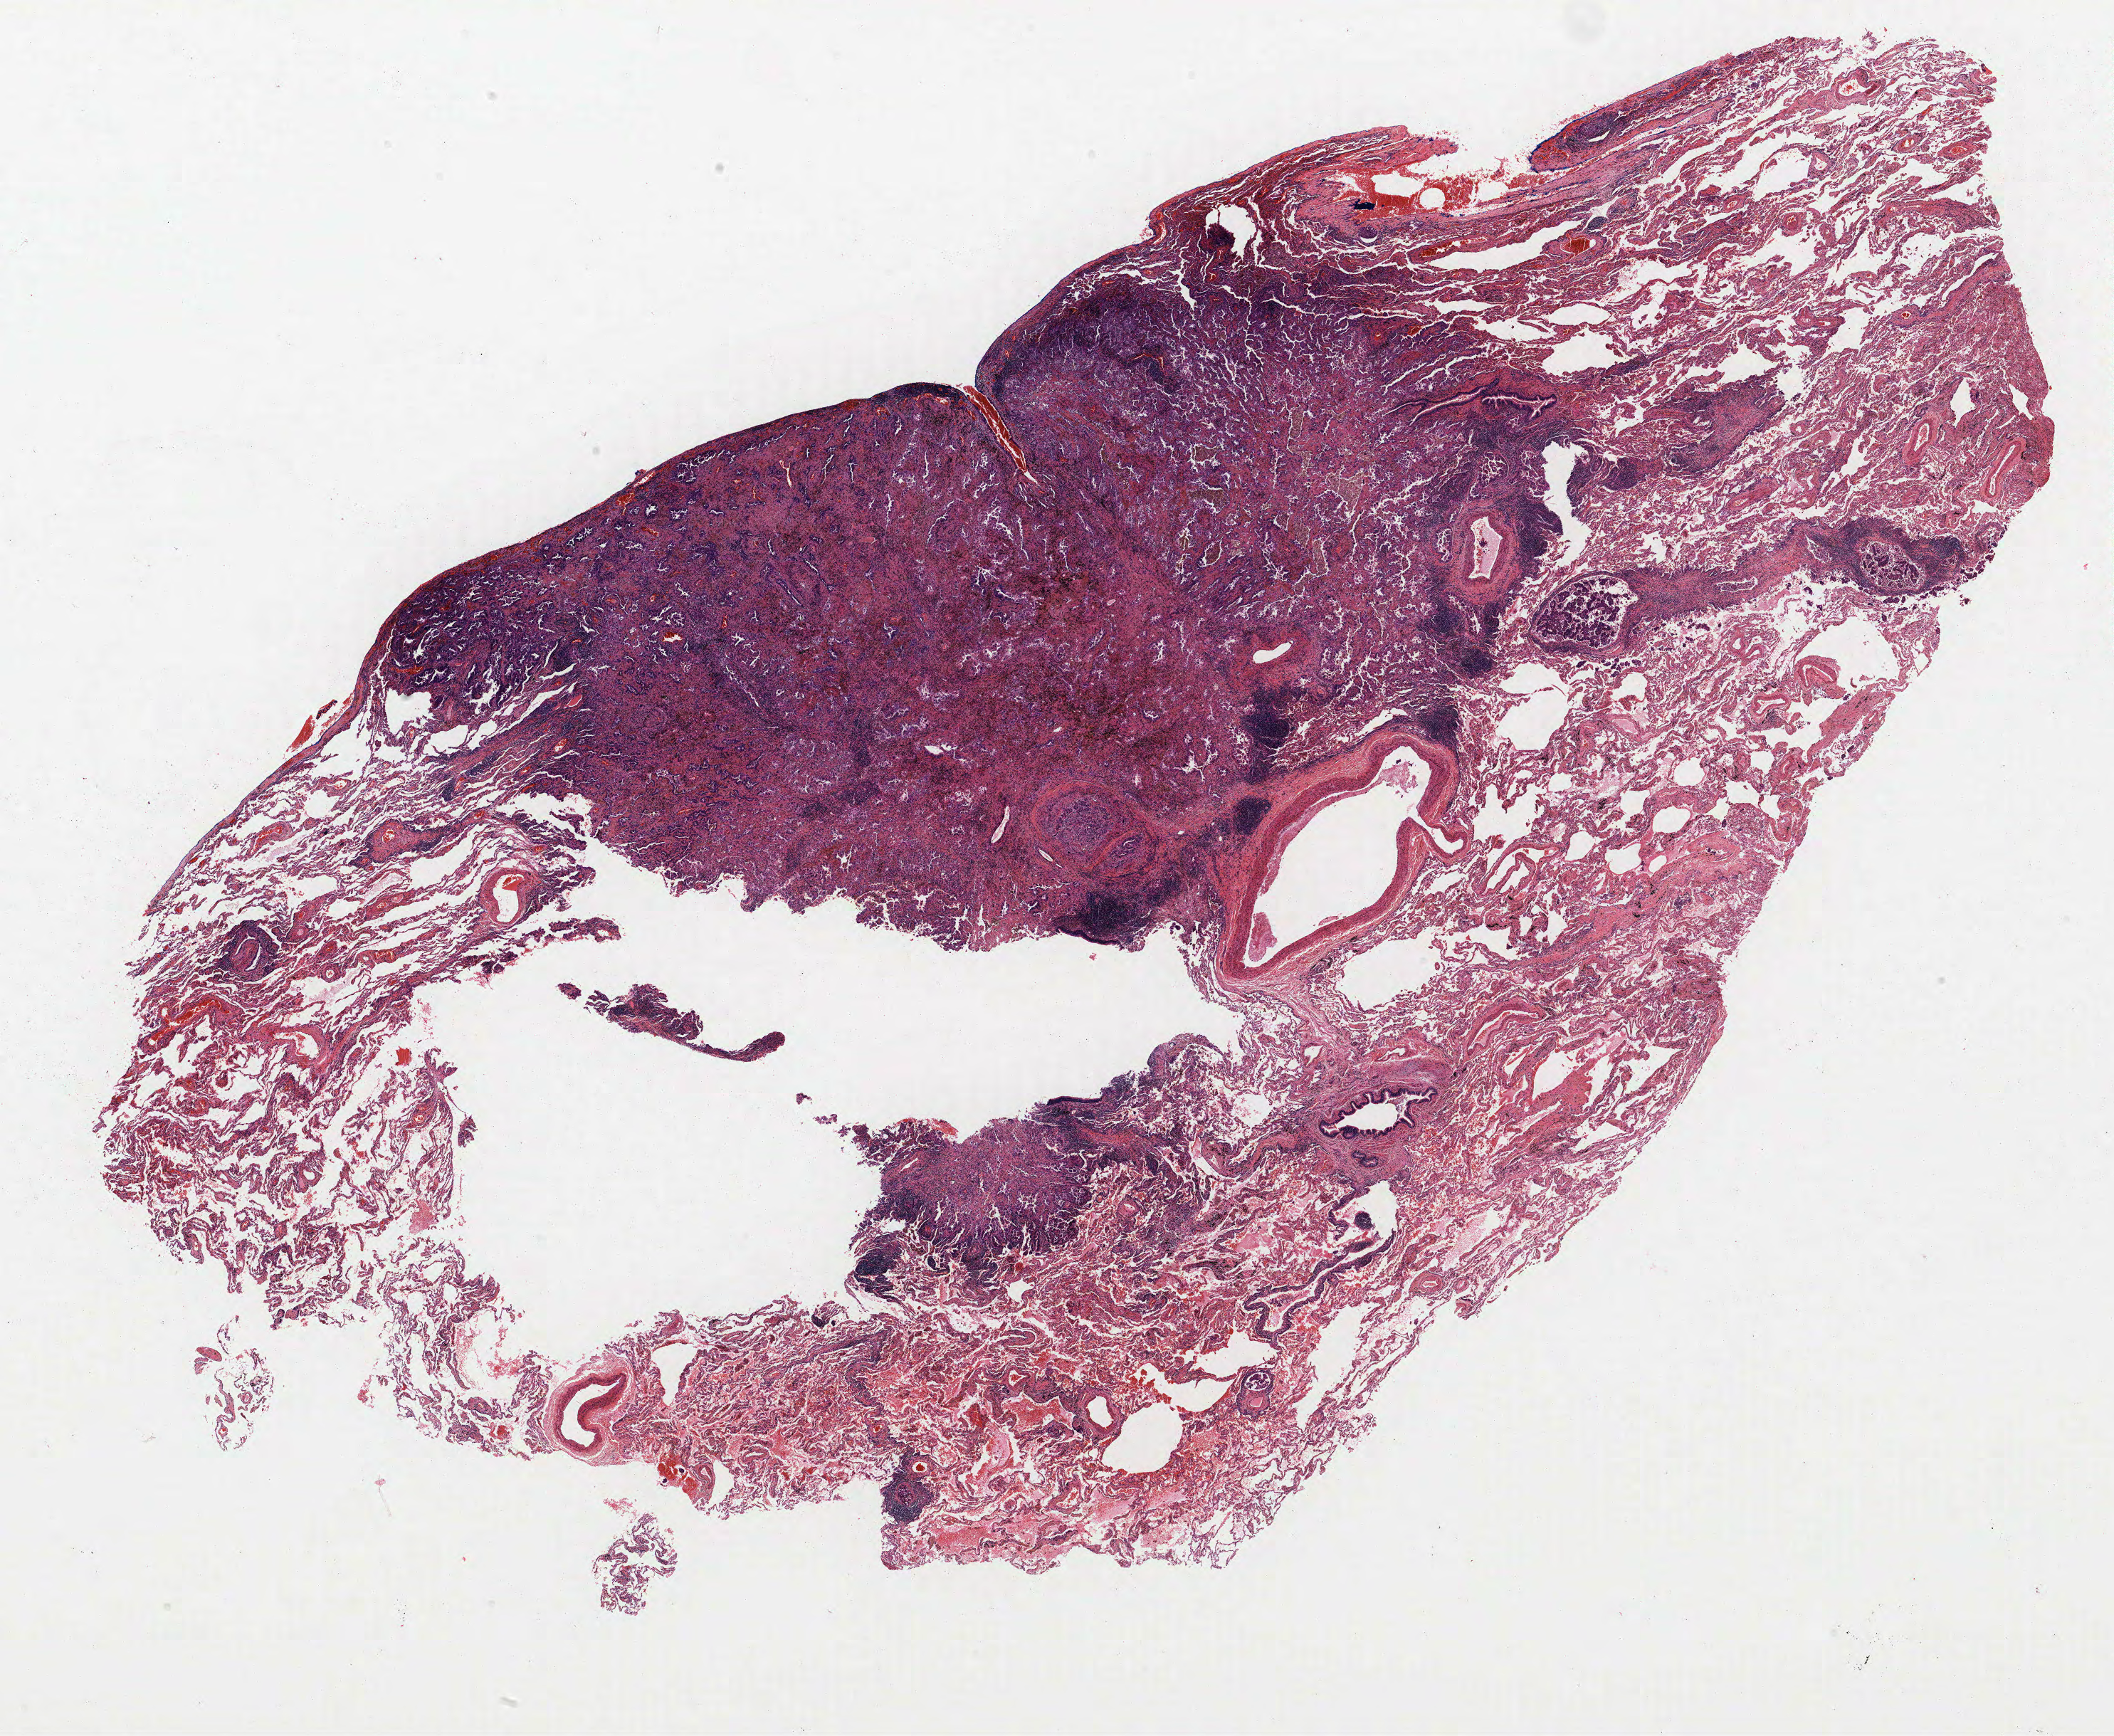
Whole-slide histology image, H&E — whole scanned area (about 23.8 x 19.5 mm) shown as a low-resolution overview, formalin-fixed paraffin-embedded (FFPE) section, lung tissue. Male, age 70 at enrolment. Current smoker at enrolment. Grade: poorly differentiated (G3).
Tumour size (pathology): 17 mm. Participant's lung-cancer diagnosis: Mixed cell adenocarcinoma. Primary tumour location (clinical record): left upper lobe. ICD-O-3 topography: upper lobe of lung (C34.1). Stage (AJCC 6th edition): IIB.